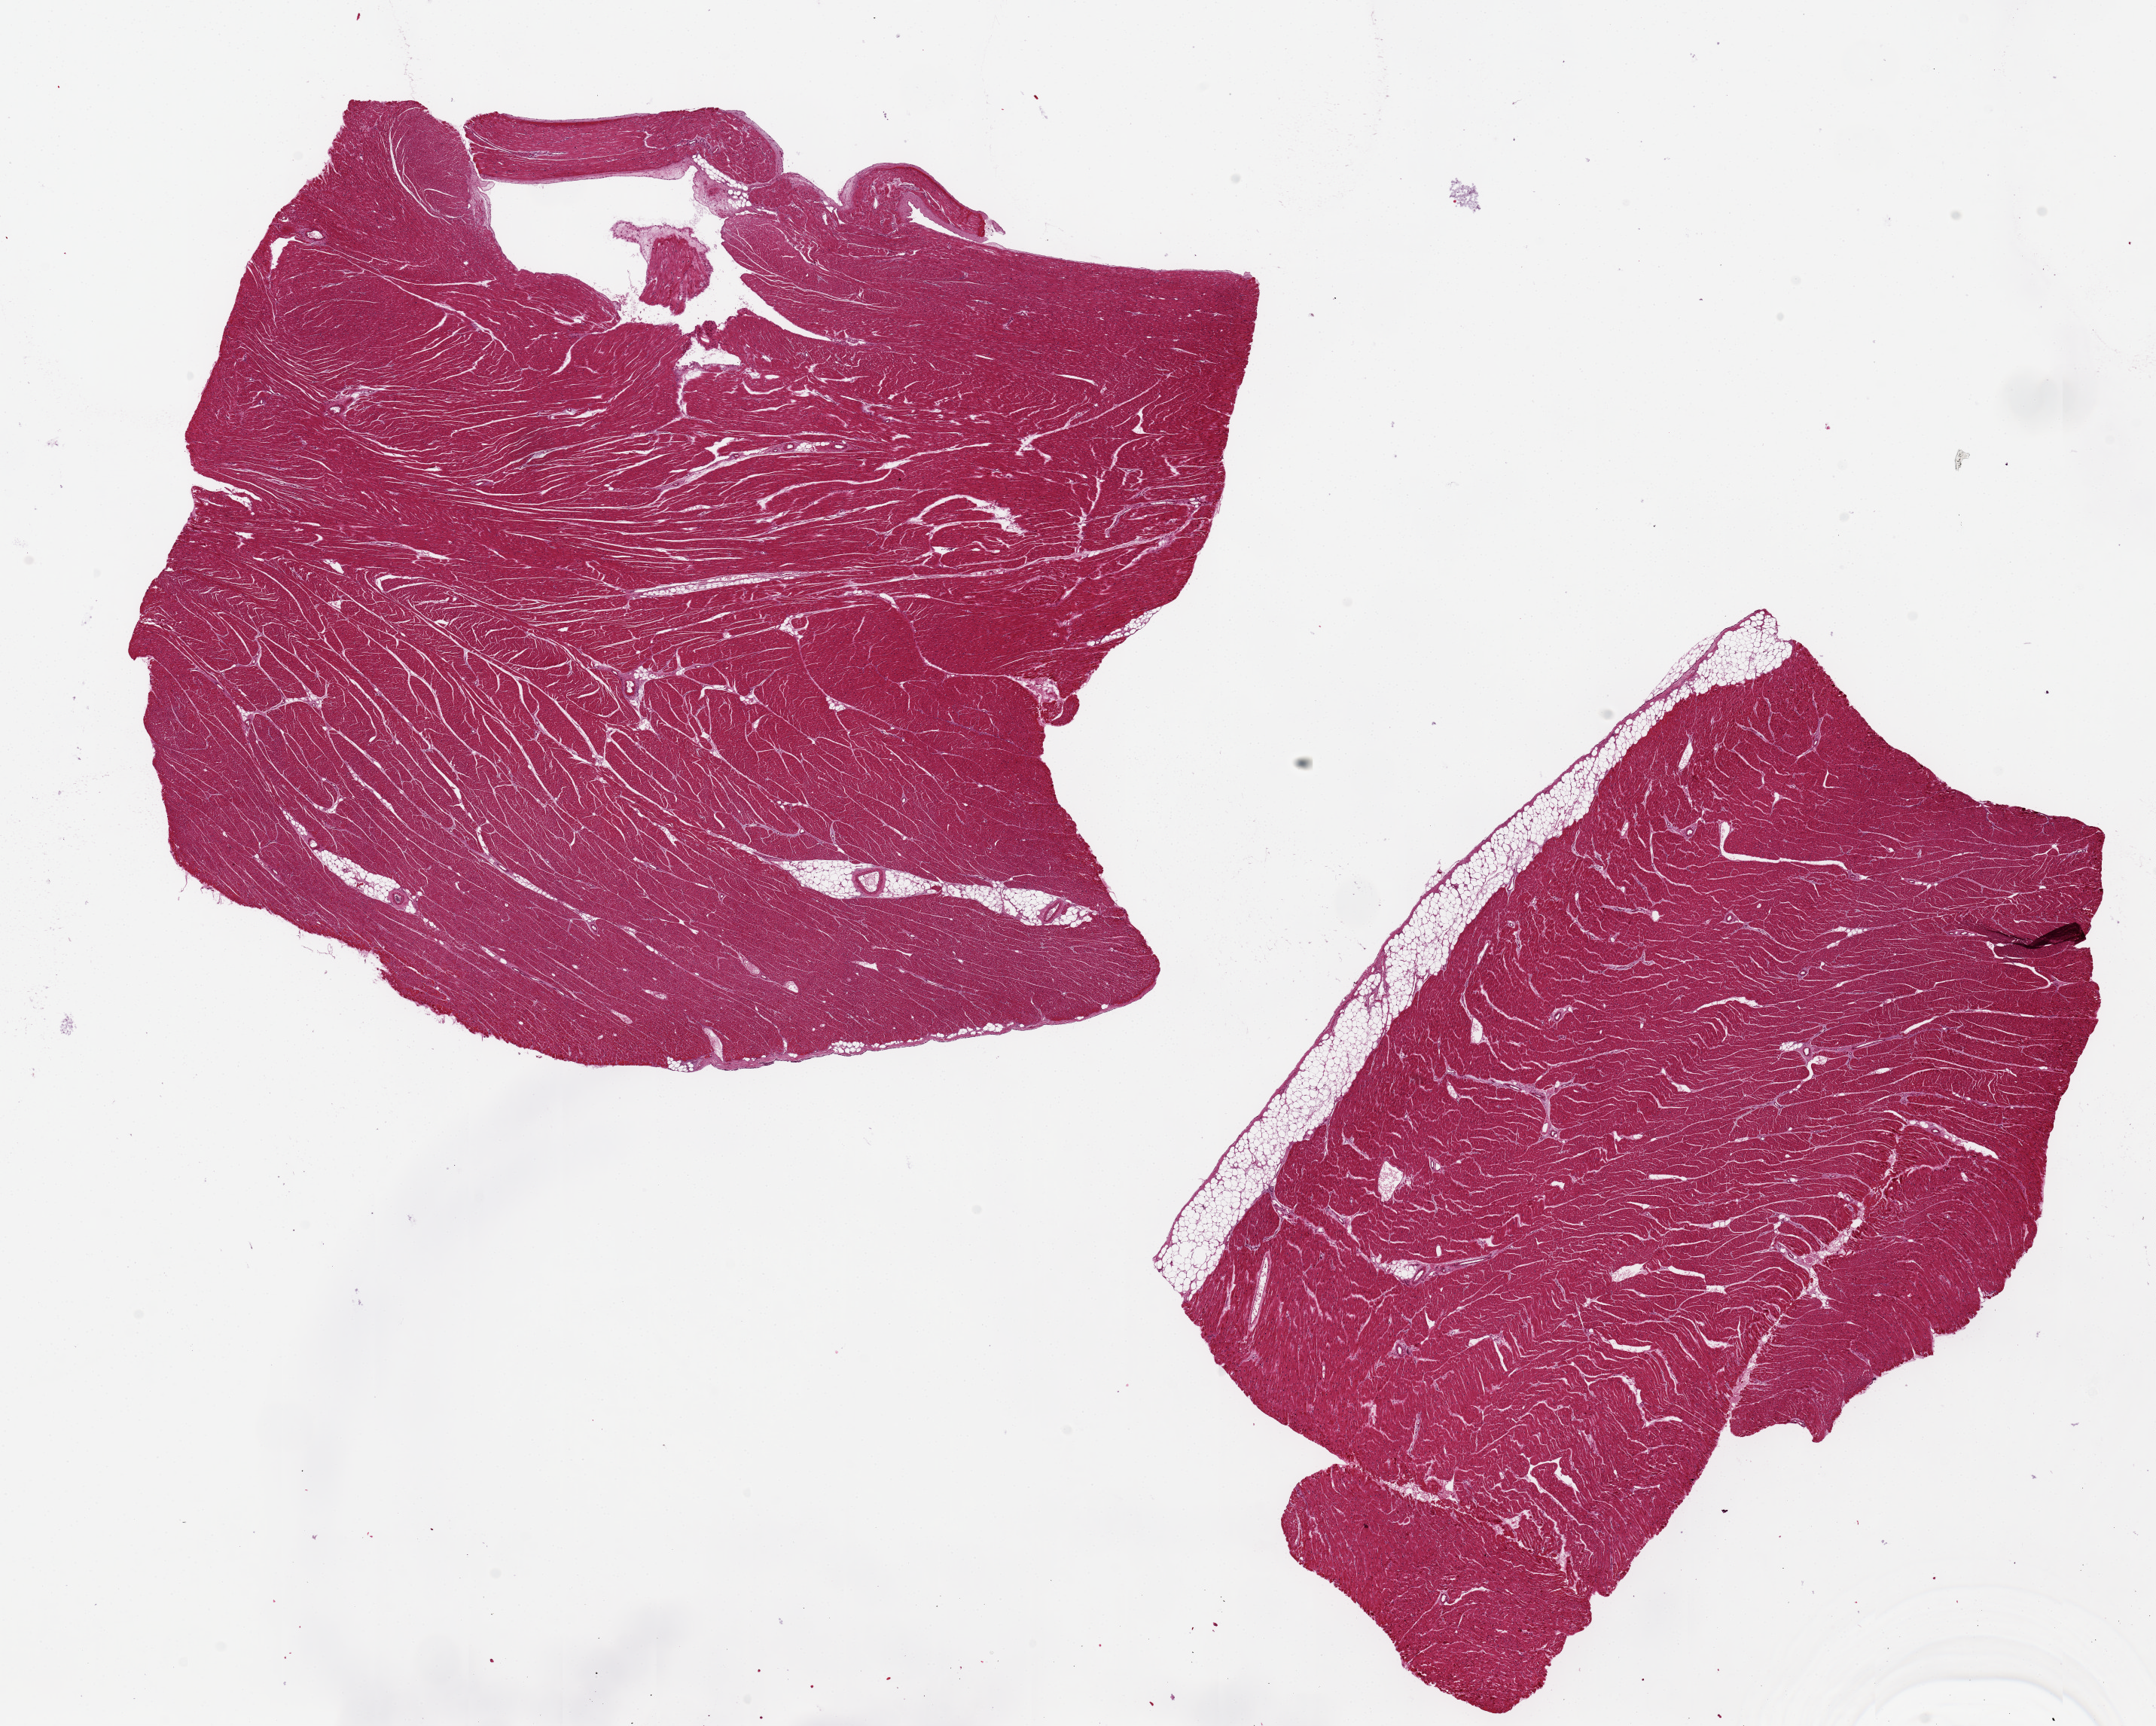
Hematoxylin and eosin (H&E) whole-slide image, whole scanned area (about 22.6 x 18.1 mm) shown as a low-resolution overview, PAXgene-fixed paraffin-embedded (PFPE) section, section of heart (target tissue), tissue donor sample. Donor sex: male.
Reviewer comment on this tissue sample: 2 pieces ~10x7mm, minimal ischemic changes.